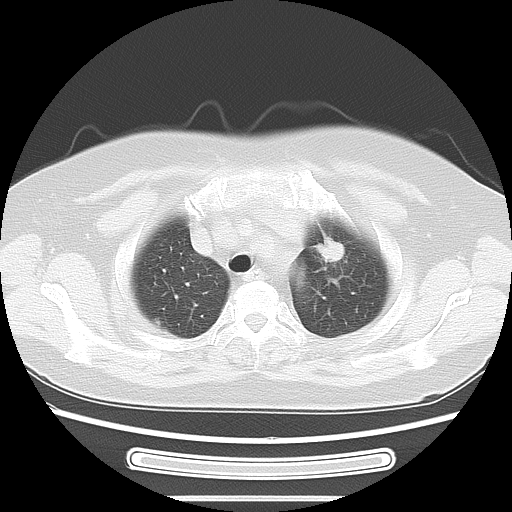
Chest CT, one axial slice. Slice 48 of 58 in the series (ordered by position). 120 kVp. Lung window (W 1500 / L -600 HU). 5 mm slice thickness. 512 × 512 image matrix, field of view 350 × 350 mm. Female patient, age 70 years. From the clinical record (not read from this slice): clinical TNM (as recorded): T1c N0 M0; histopathological grade: G2-3.
Structures marked on this image (bounding box drawn by a radiologist):
- lung tumour (recorded histology: adenocarcinoma): bounding box (x1, y1, x2, y2) in pixels: (307, 230, 347, 268)